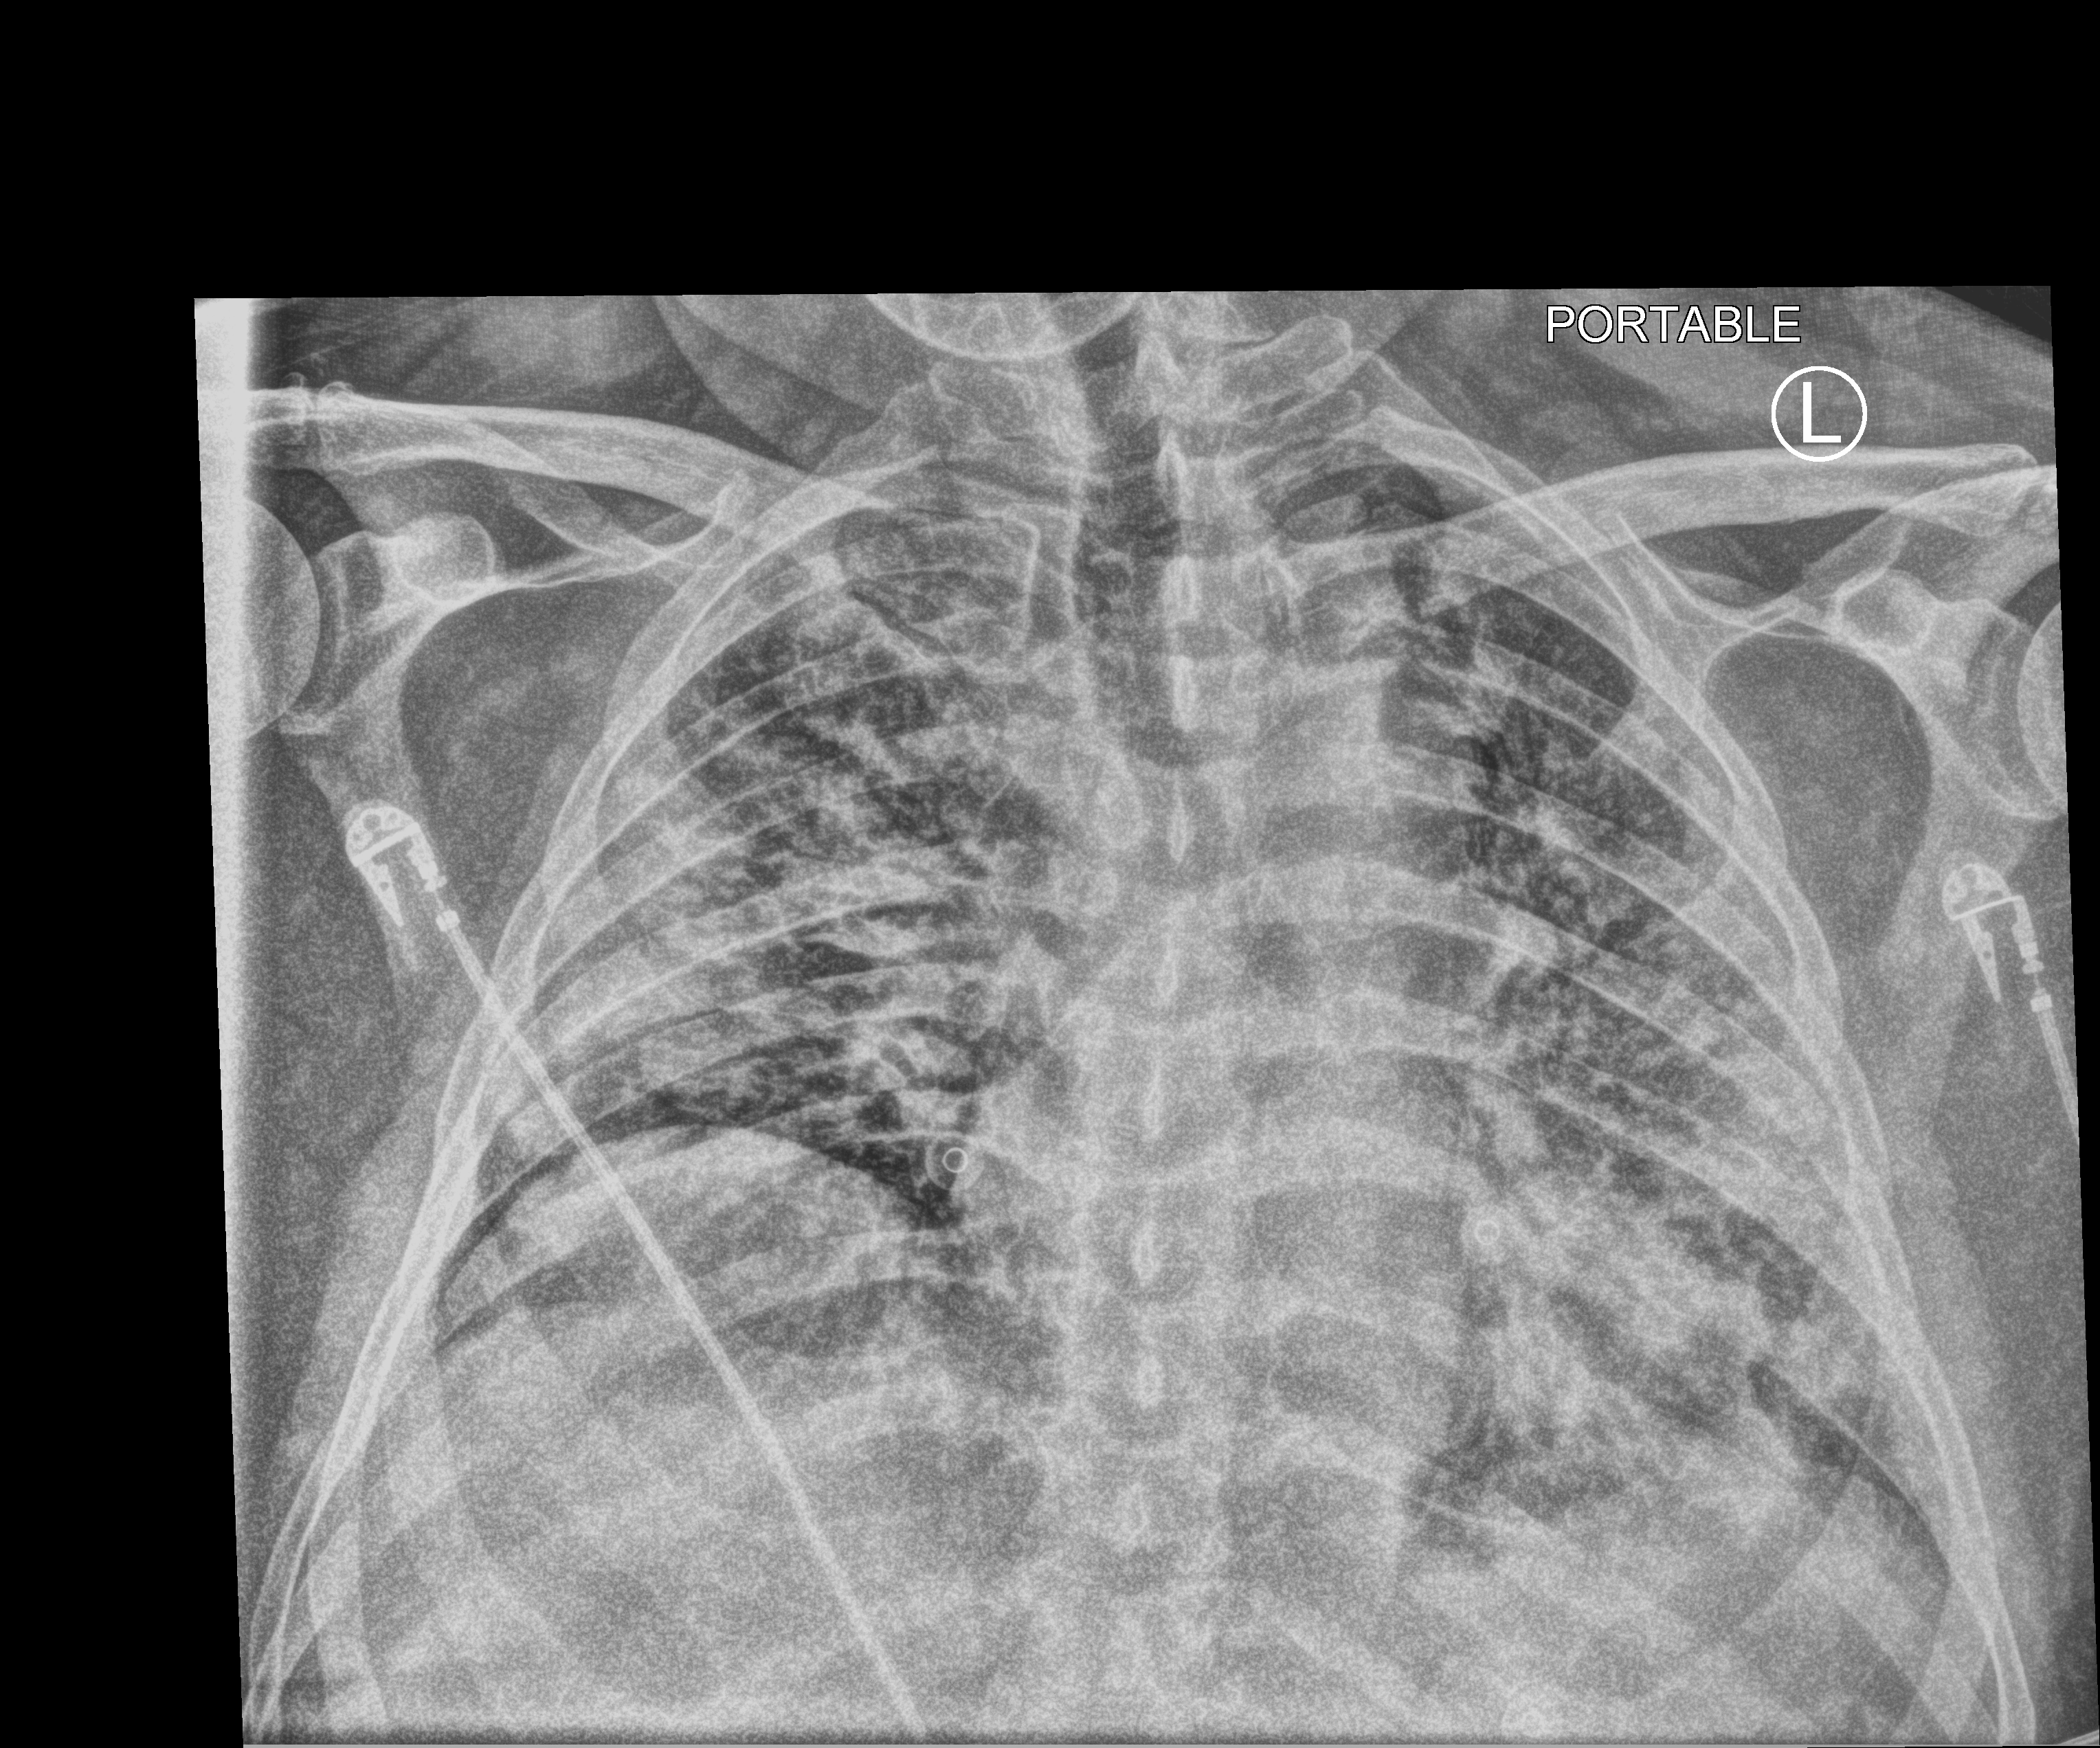
Portable chest radiograph; anteroposterior (AP) projection. Male patient hospitalised with COVID-19, age 60–74 years.
Hospital-stay facts (about this admission, not read from this image; timing relative to this image not recorded): admitted to intensive care during this hospital stay: yes.